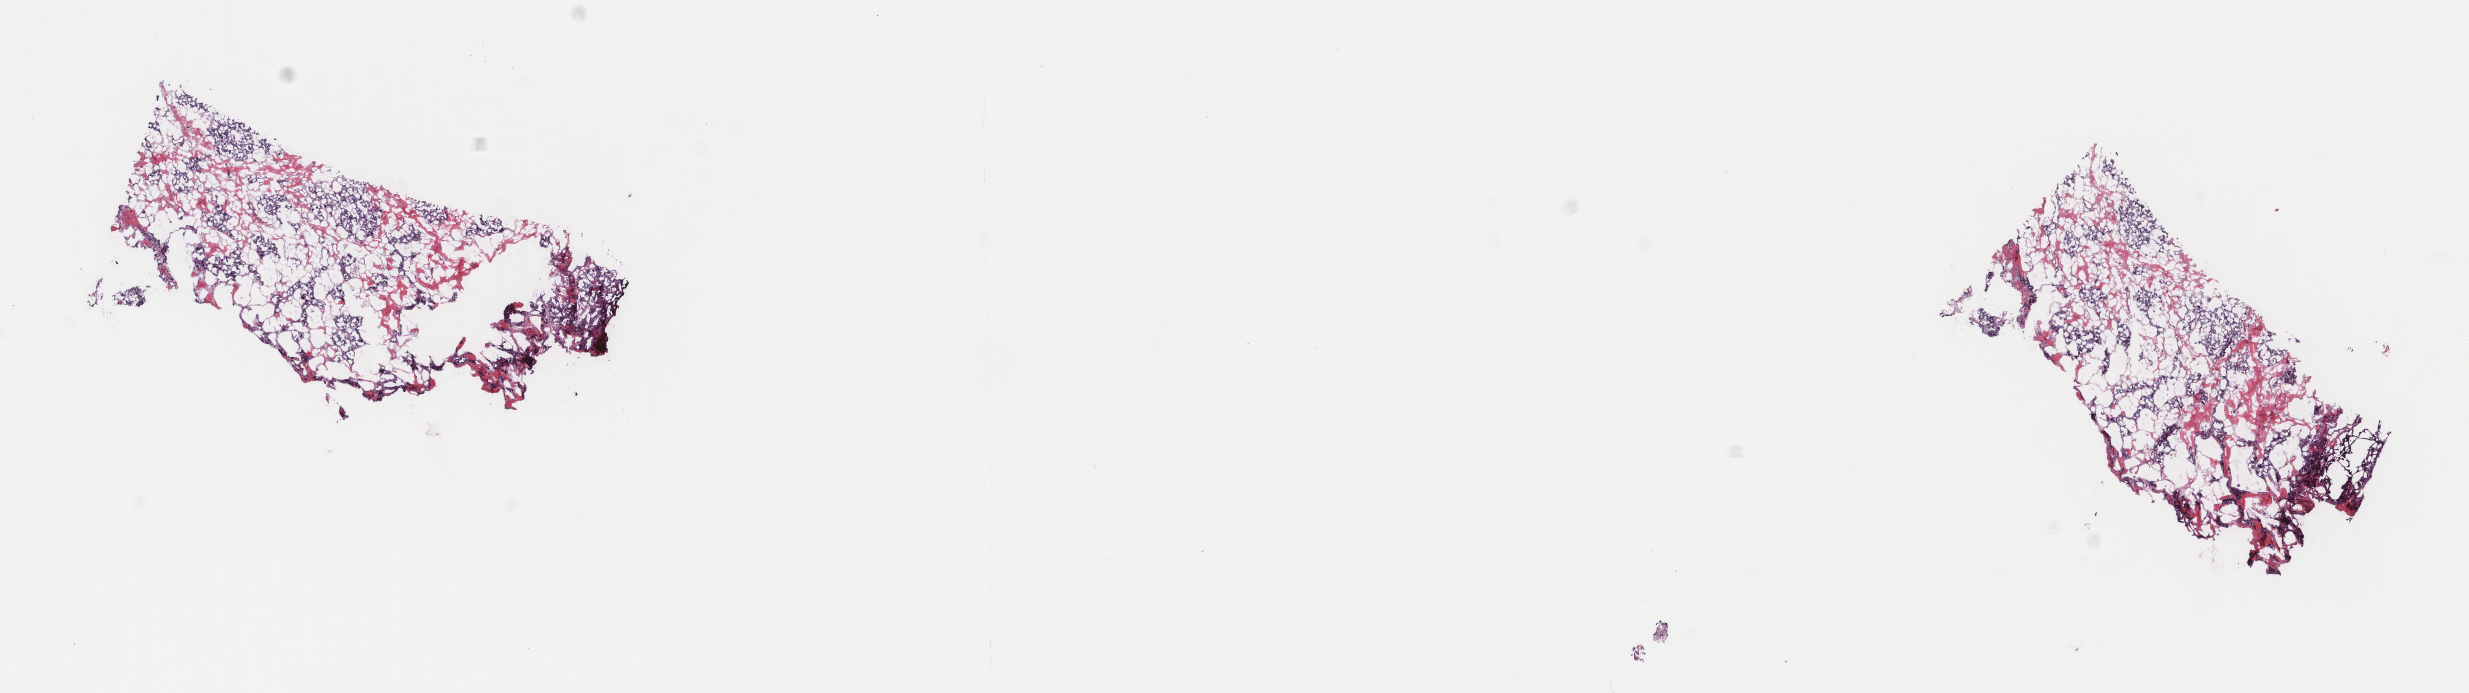
Whole-slide histology image, H&E-stained — a low-resolution overview of the entire scanned area, about 19.6 x 5.5 mm (acquisition: 40x scan), frozen section from the top of the tissue portion, primary tumour sample from the adrenal gland. Patient: male, age at initial diagnosis 47 years.
Histologic diagnosis: Pheochromocytoma, NOS.